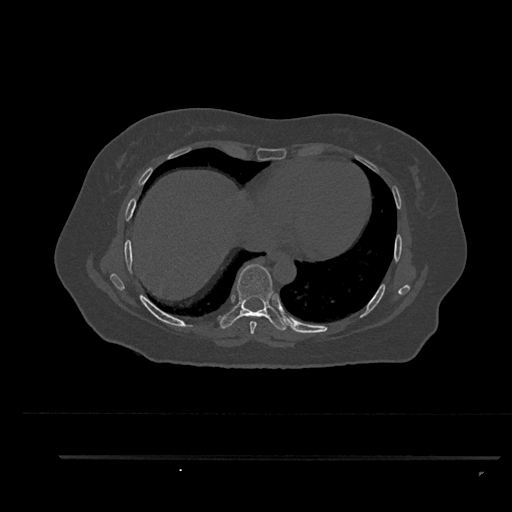
CT including the spine, one axial slice; position 472 of 797 along the scan axis; reconstruction kernel Br40s/3; 120 kVp; bone window (W 1800 / L 400 HU); 0.5 mm slice thickness; 512 × 512 image matrix, field of view 408 × 408 mm. Female patient, age 44 years. Case-level facts recorded for this patient, not image findings: primary cancer: renal.
Annotated regions visible in this slice (semi-automatic segmentation, software-assisted and operator-edited):
- T7 vertebra: box from (x=249, y=321) to (x=257, y=334) px
- T8 vertebra: (x=218, y=264)–(x=287, y=331)